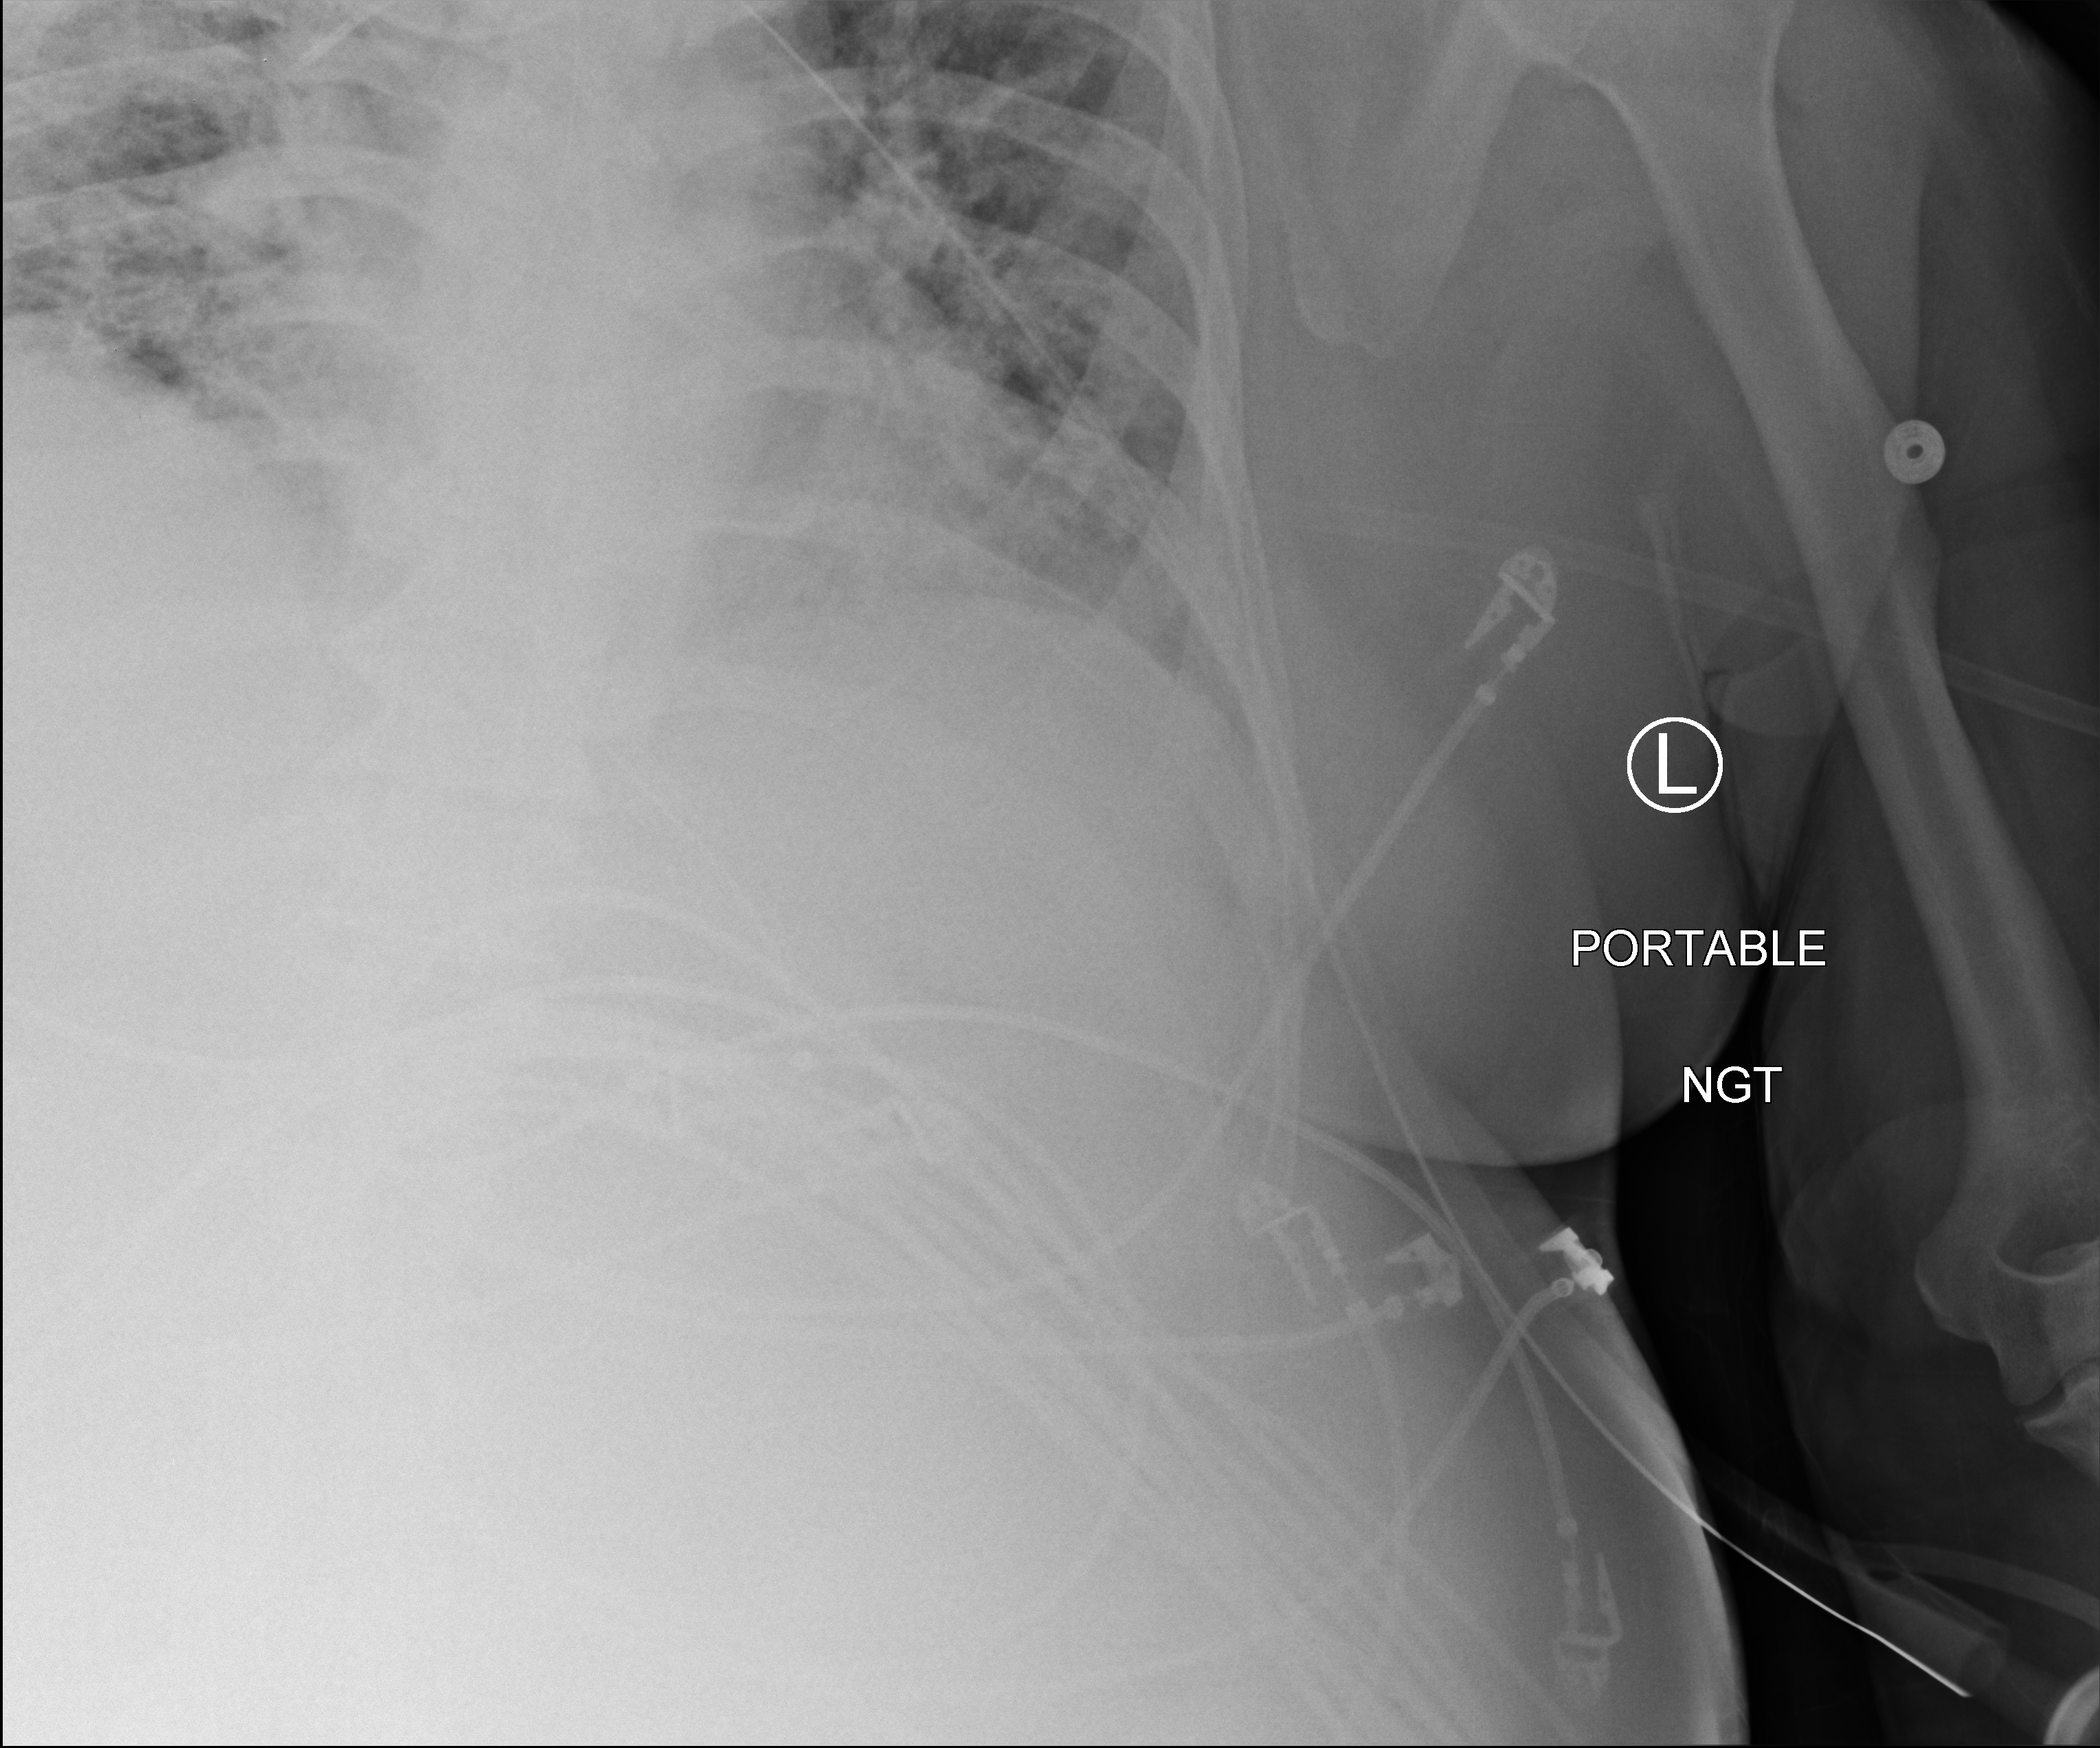
Chest X-ray (portable); anteroposterior (AP) projection. Male patient hospitalised with COVID-19, age 18–59 years.
From the hospital-stay record, not from the radiograph (when in the stay this image was taken is not recorded): length of hospital stay: 47 days; mechanically ventilated during this hospital stay: yes.